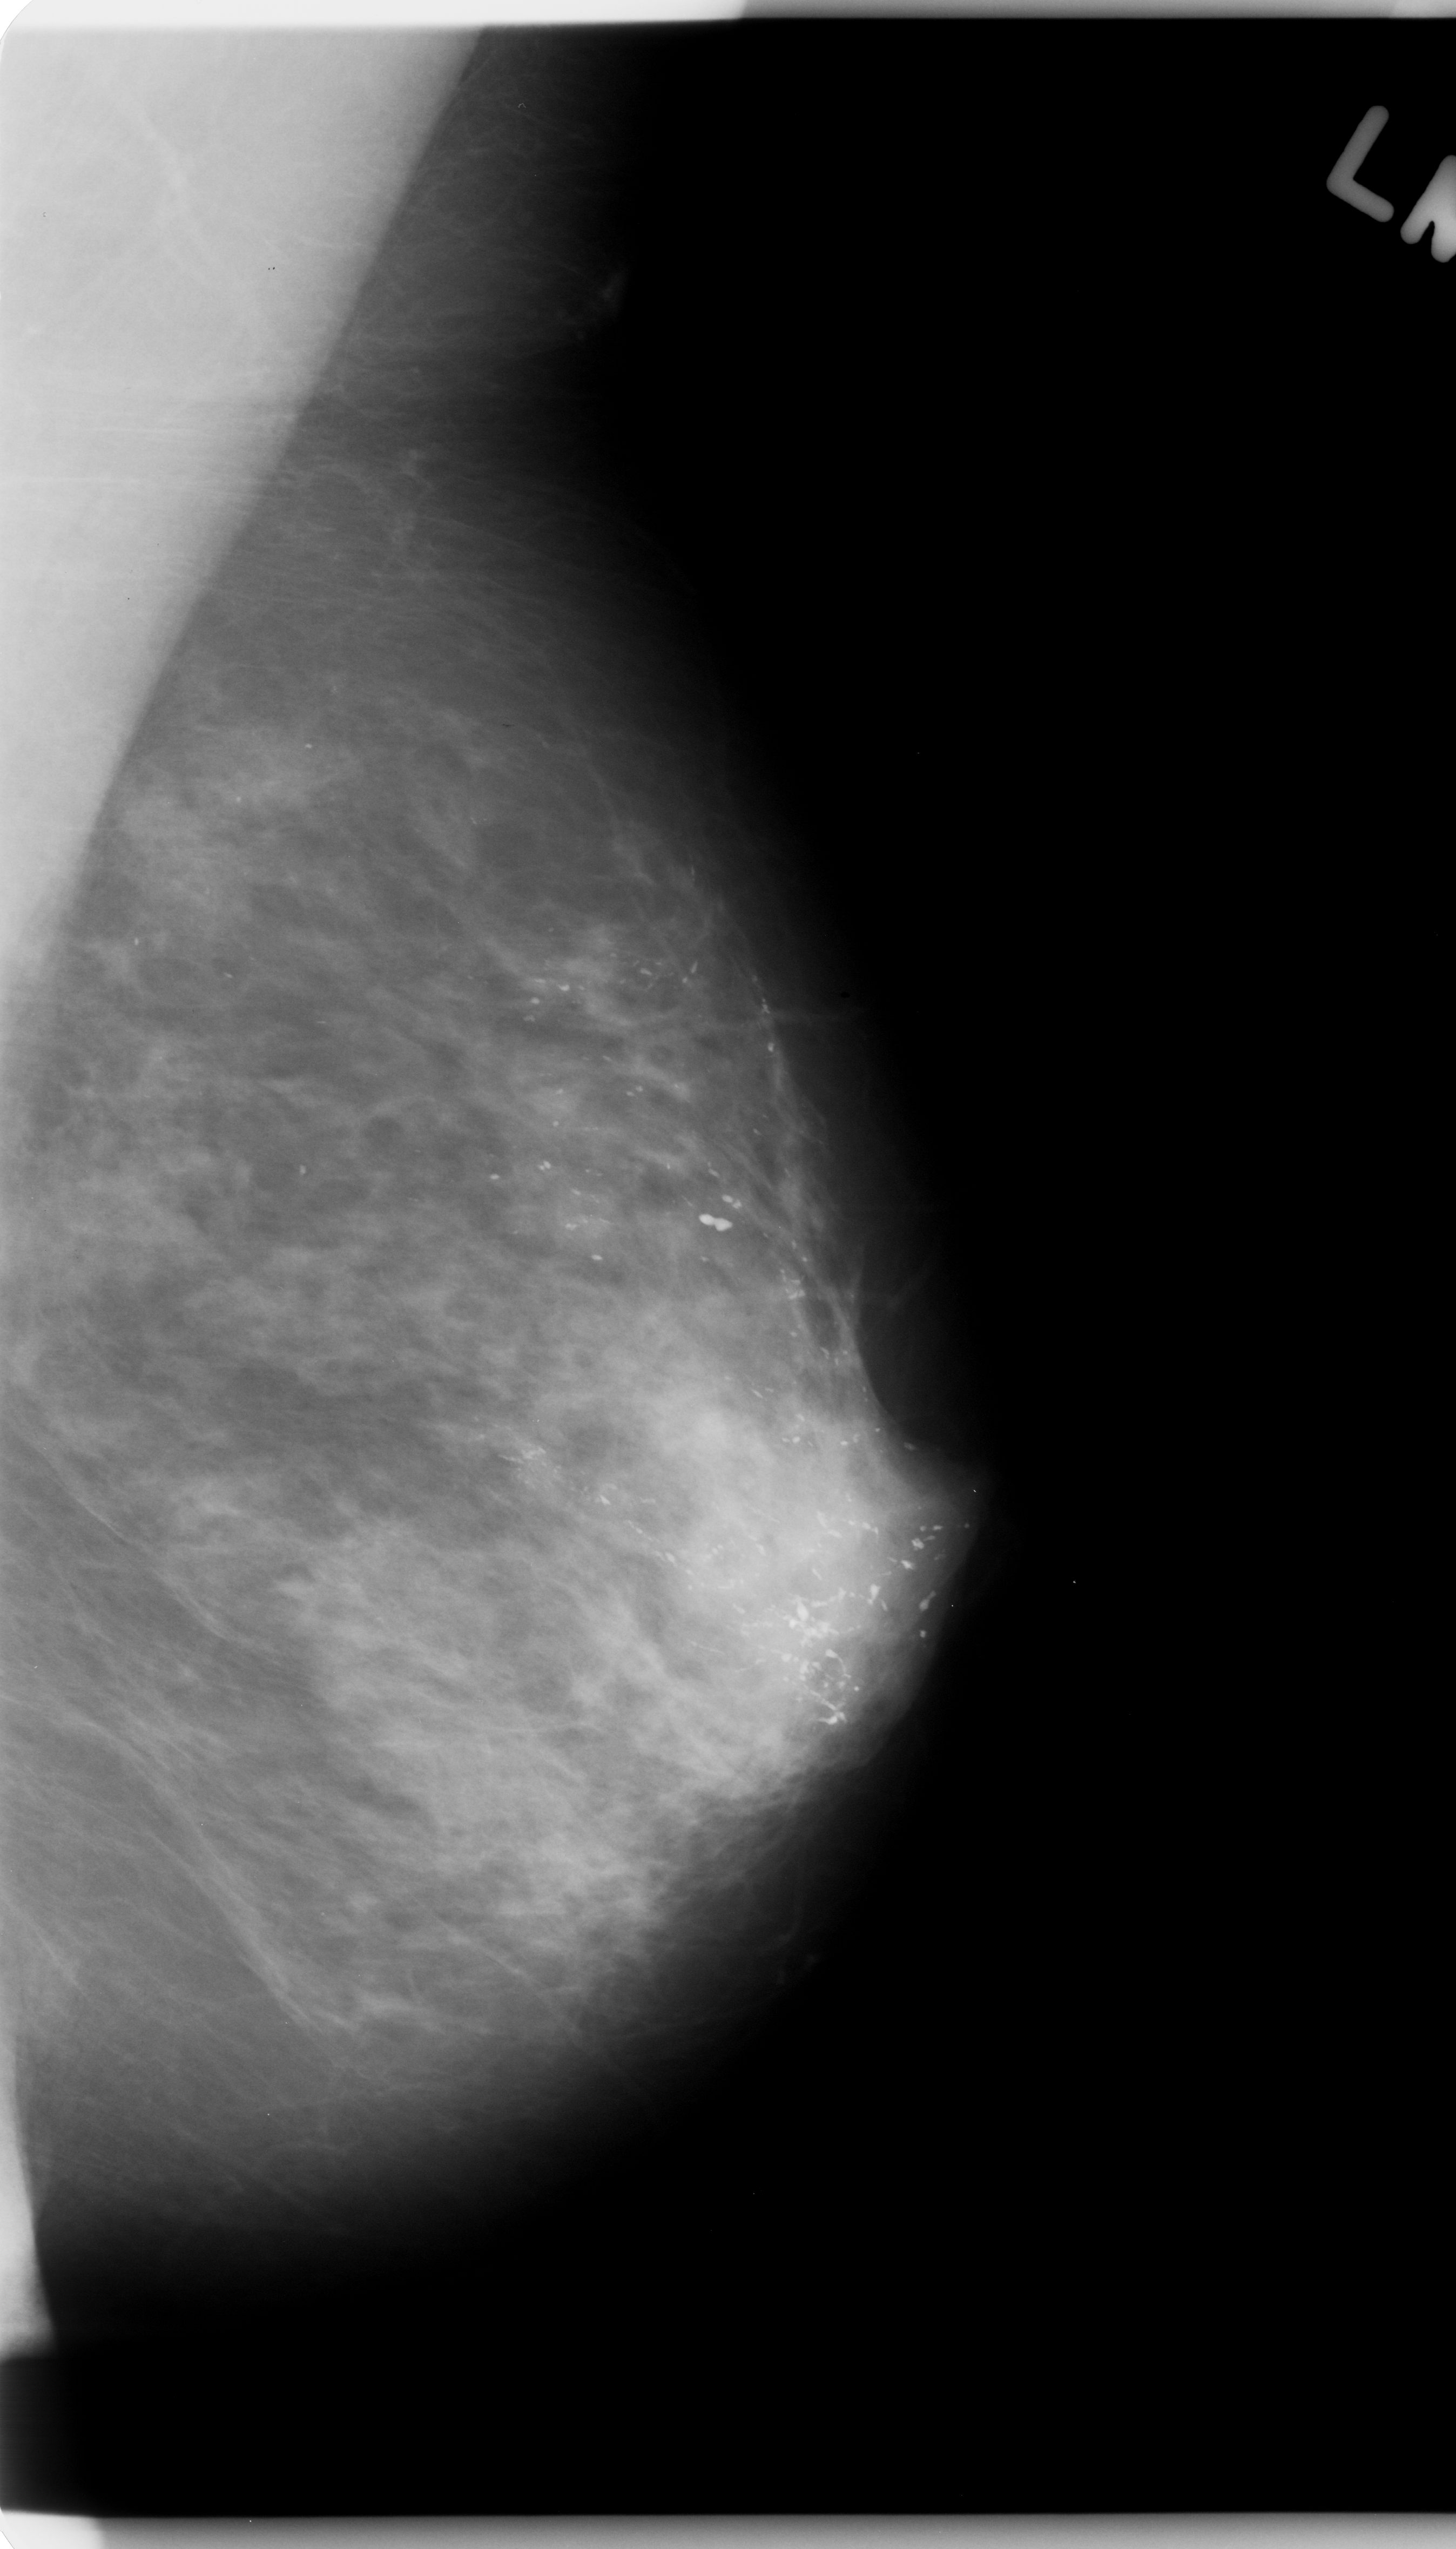
Digitized screen-film mammogram; left breast; mediolateral oblique (MLO) view; breast composition: heterogeneously dense (BI-RADS density category 3 of 4); 1456 × 2549 image matrix.
Expert-marked regions of interest on this image (one box per marked abnormality):
- calcifications, morphology fine linear branching, distribution regional; BI-RADS assessment category 5; pathology result (as recorded, not read from the image): malignant: bounding box <56,643,1003,1867> (left, top, right, bottom; pixels)